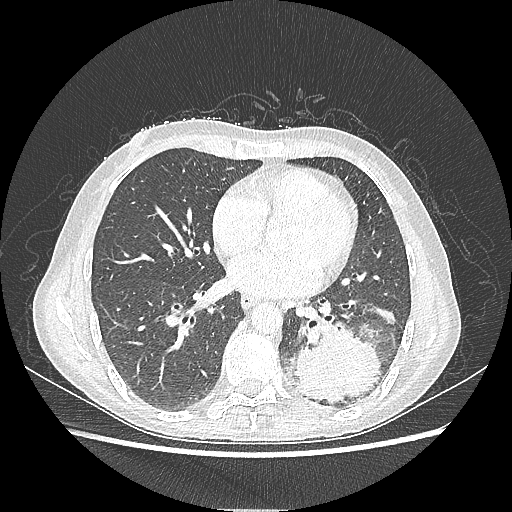
Chest CT, one axial slice. Position 96 of 220 along the scan axis. Lung window (W 1500 / L -600 HU). 1.25 mm slice thickness. 512 × 512 image matrix, field of view 360 × 360 mm. Female patient, age 53 years. Case-level facts recorded for this patient, not image findings: clinical TNM (as recorded): T3 N0 M0.
Outlined on this slice (bounding box drawn by a radiologist):
- lung tumour (recorded histology: adenocarcinoma): bounding box <288,321,383,406> (left, top, right, bottom; pixels)